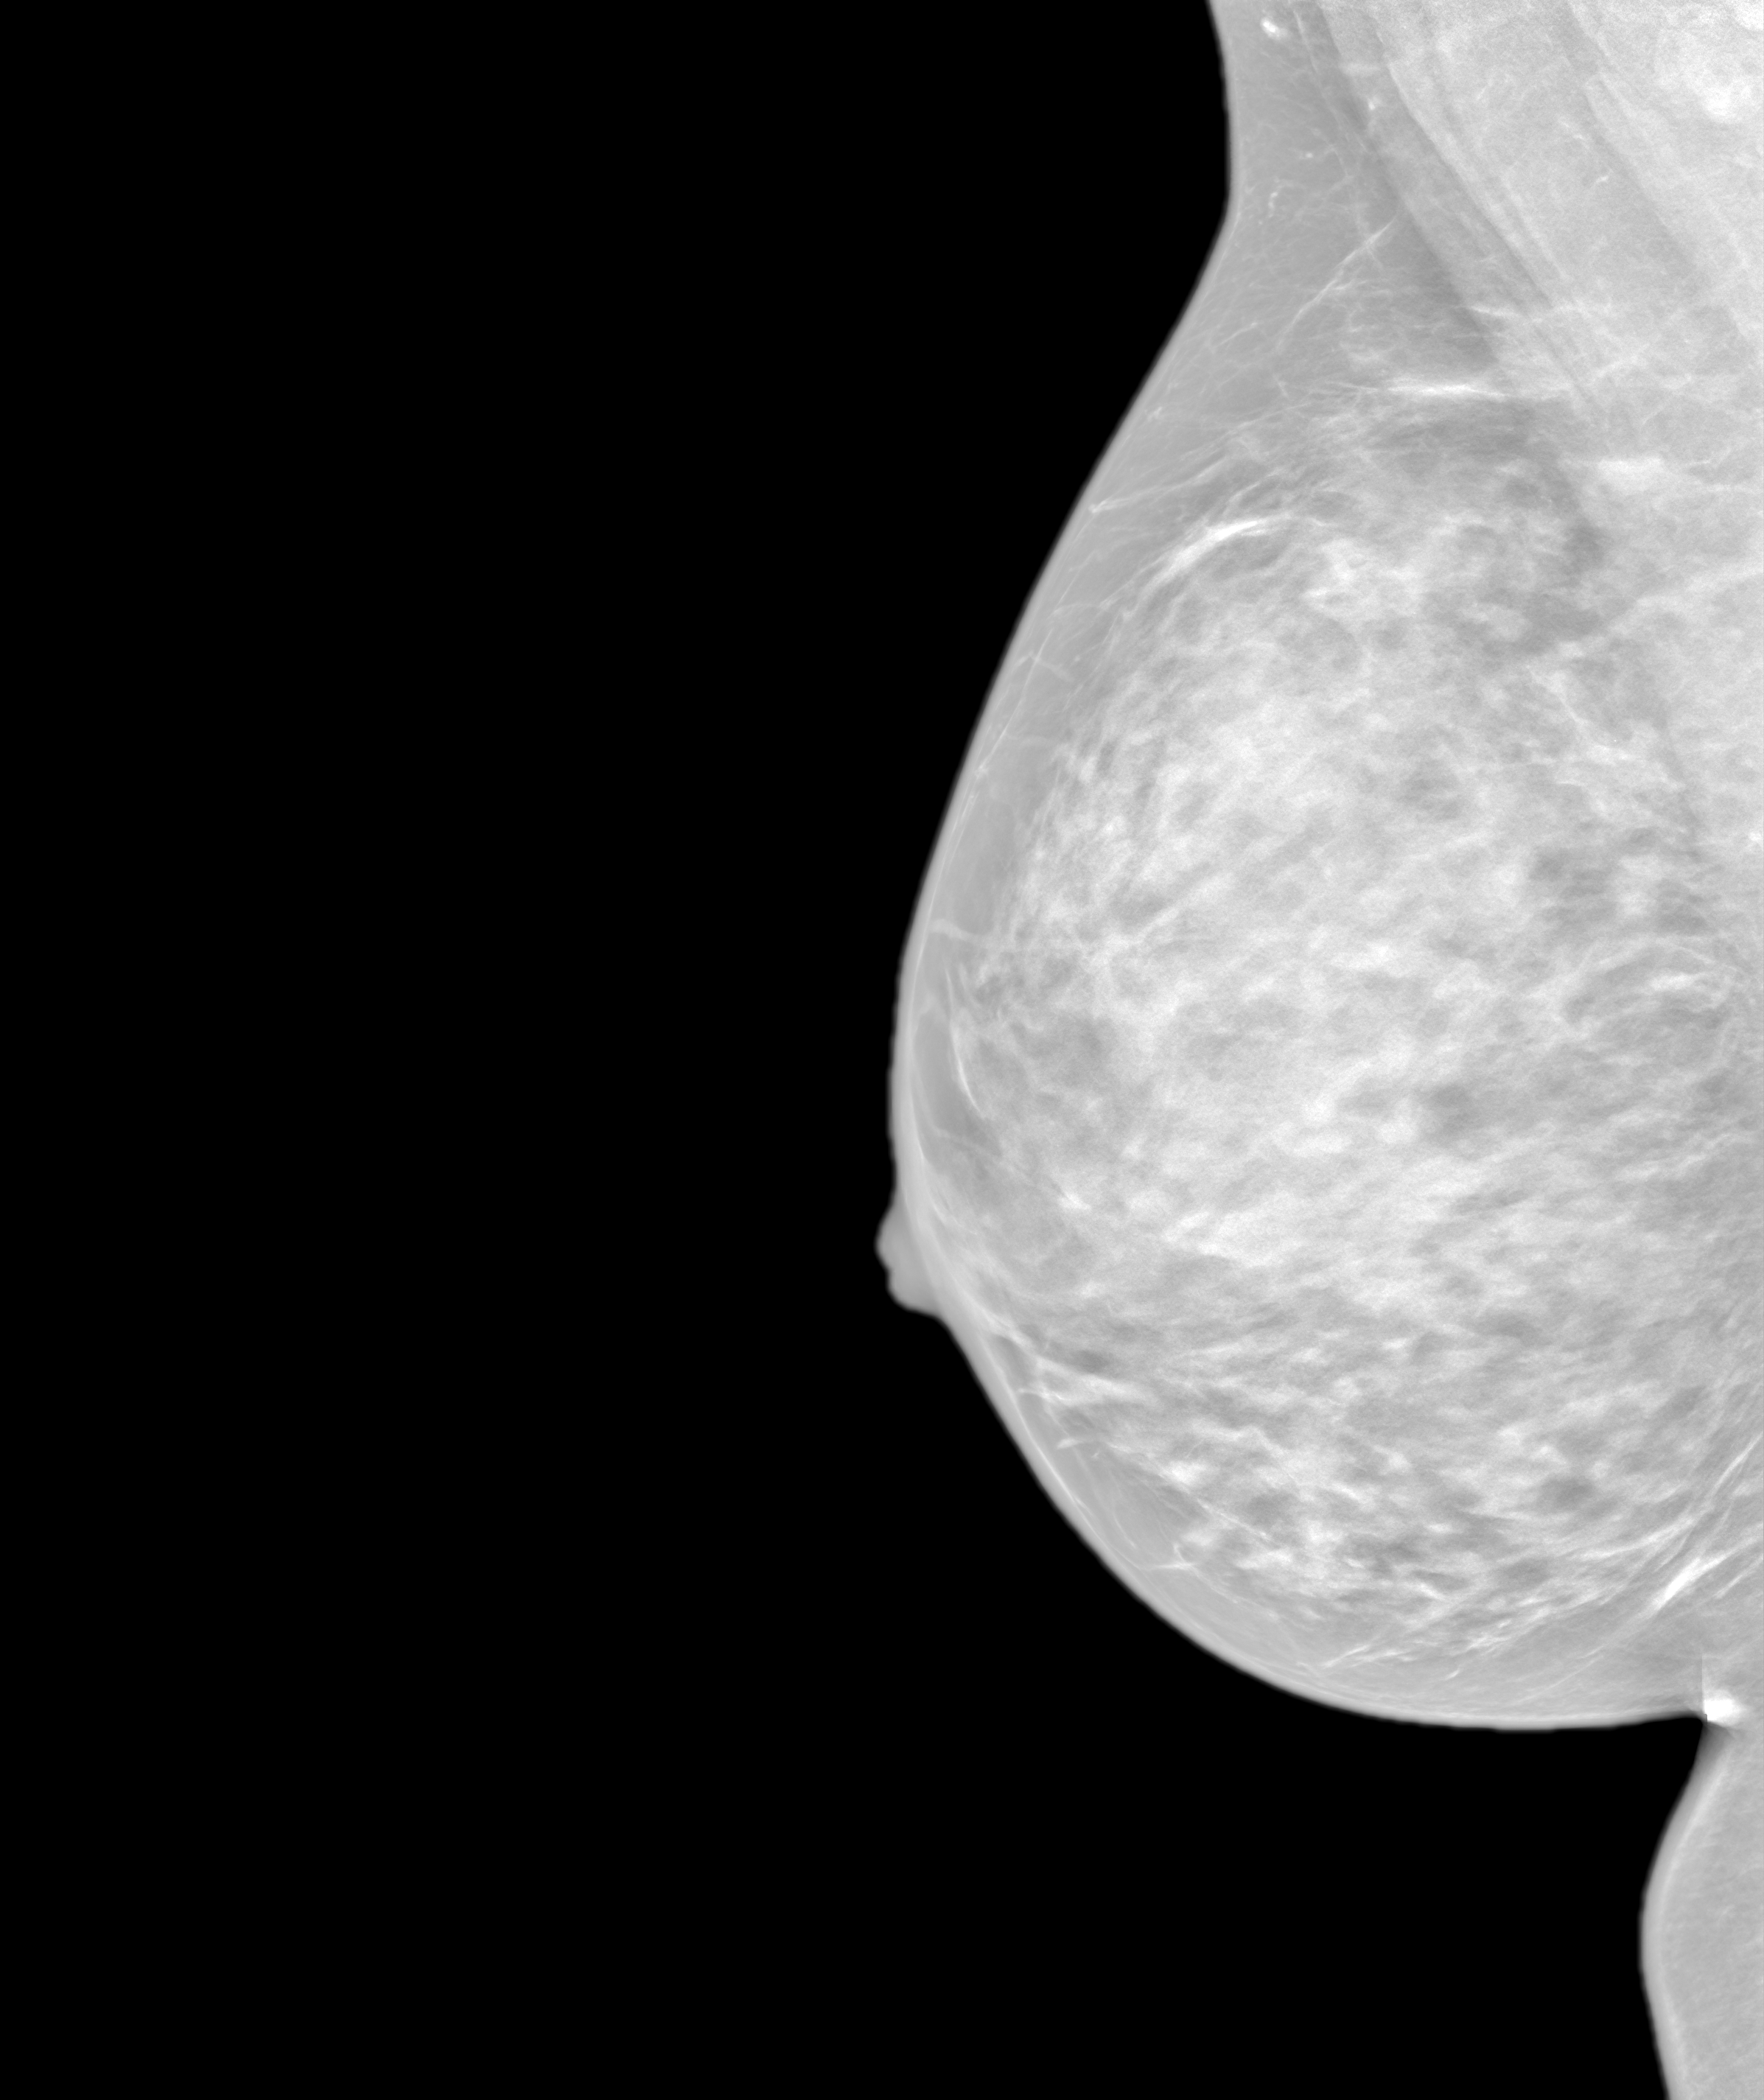
Synthetic 2-D view generated from a tomosynthesis acquisition (not an FFDM exposure); right breast; mediolateral oblique (MLO) view; screening examination. Patient: female, 42 years.
BI-RADS breast density category at the screening exam (both breasts, scale 1–4): 4. Final BI-RADS category for the screening round (tomosynthesis exam, both breasts): category 1. Recall: no recall after this screen.